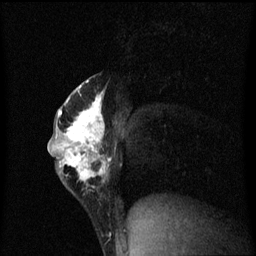
Breast MRI (dynamic contrast-enhanced), one sagittal slice. Position 33 of 60 along the scan axis. Dynamic contrast-enhanced series, image 2 of 3 at this slice position (ordered by acquisition). 1.5 T. TE 4.2 ms, TR 8.4 ms. 256 × 256 image matrix. Patient: female, 40 years.
Outlined on this slice (semi-automatic segmentation, software-assisted and operator-edited):
- analysis volume of interest (the breast-tissue region the enhancement analysis was run in; not a lesion): bounding box [x1, y1, x2, y2] px = [49, 76, 113, 199]
- tumour enhancement mask (voxels above the 70 % enhancement threshold inside the analysis volume of interest): [49, 80, 113, 189]